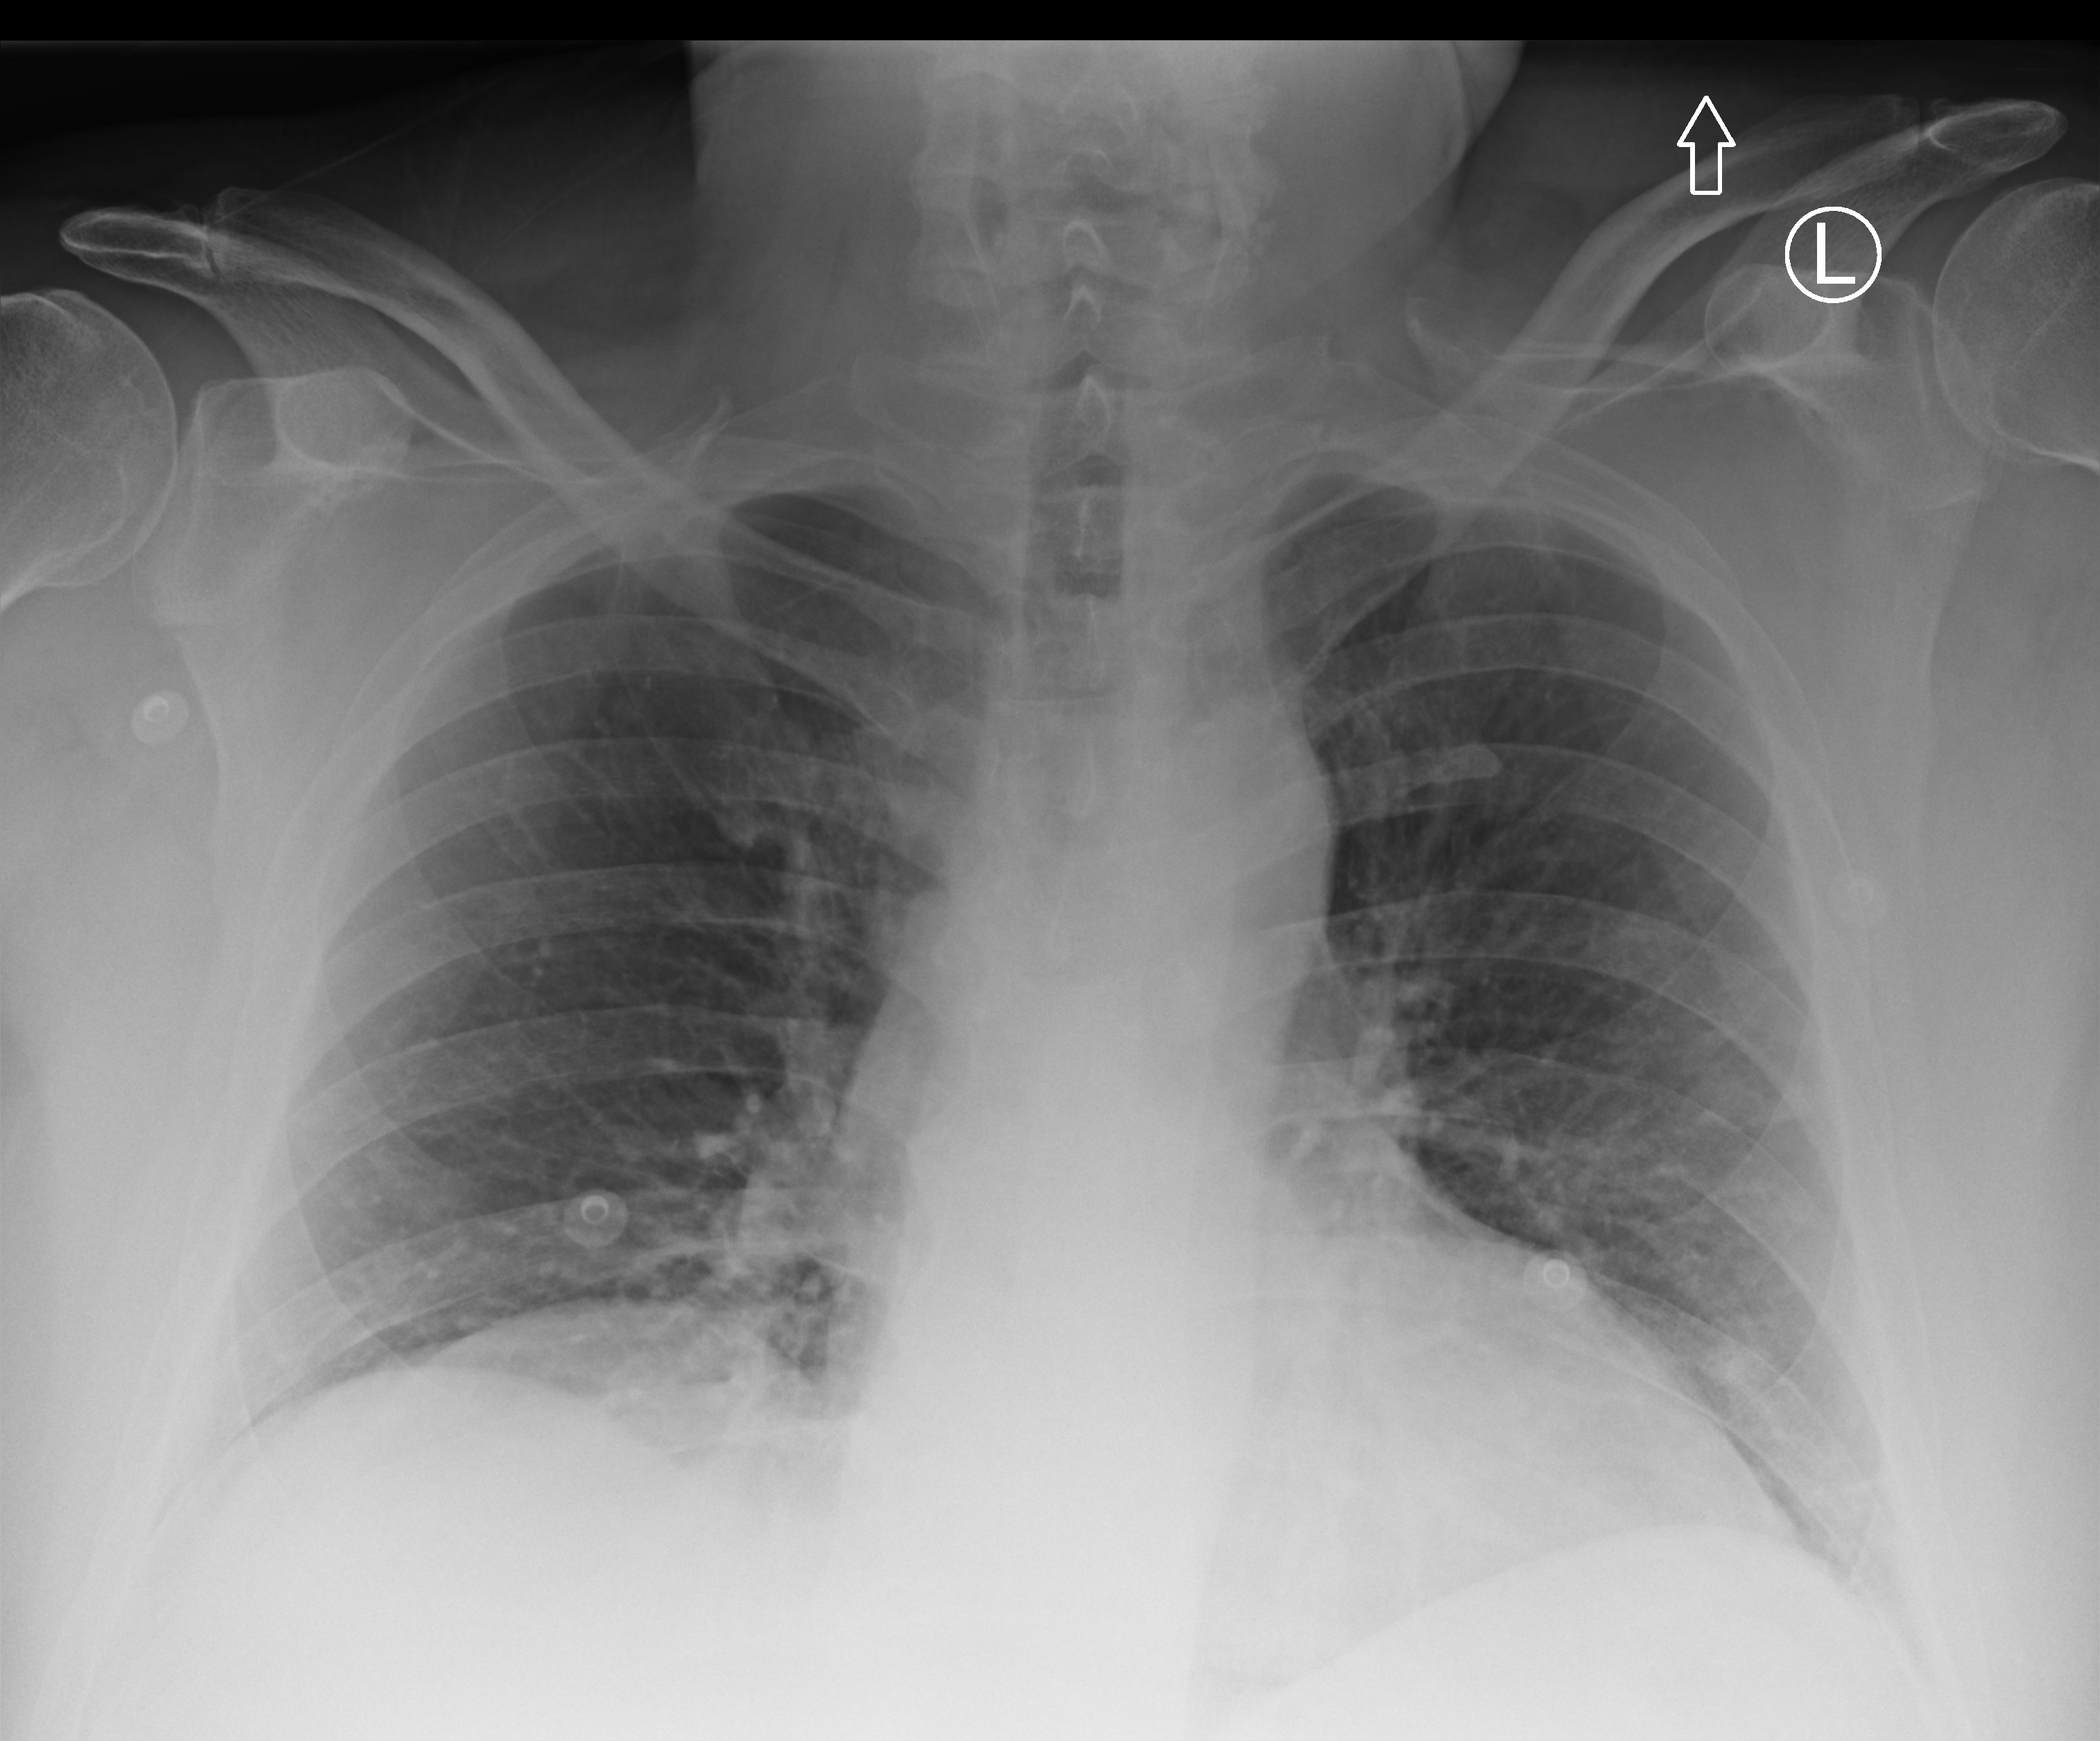
Portable chest radiograph, anteroposterior (AP) projection. Patient hospitalised with COVID-19; male, aged 18–59 years.
Admission-level facts for this patient (not findings on this image; timing relative to this image not recorded):
- mechanically ventilated during this hospital stay: no